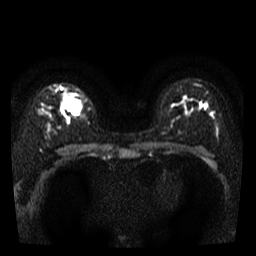
Breast MRI, one axial slice. Slice 24 of 40 in the series (ordered by position). Diffusion-weighted series; image 2 of 4 stored at this slice position (different b-values; order by instance number). 3 T. 5 mm slice thickness. 256 × 256 image matrix. Female patient.
Outlined on this slice (manually delineated by an expert):
- tumour on diffusion-weighted imaging: bounding box <65,100,80,112> (left, top, right, bottom; pixels)